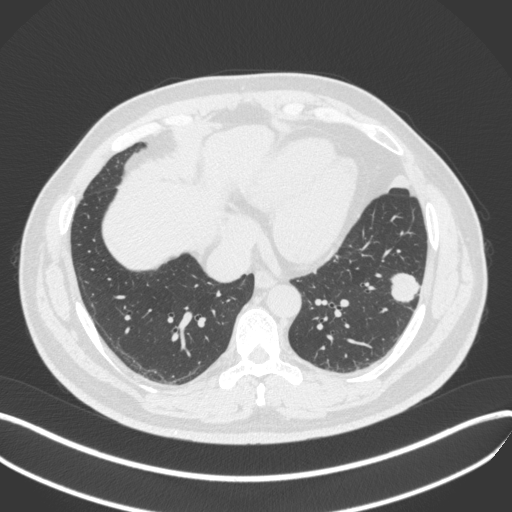
Chest CT, one axial slice; 120 kVp; lung window (W 1500 / L -600 HU); 1 mm slice thickness; 512 × 512 image matrix, field of view 400 × 400 mm. Male patient, age 39 years. Case-level facts recorded for this patient, not image findings: clinical TNM (as recorded): T2a N0 M0; histopathological grade: G2-3.
Outlined on this slice (bounding box drawn by a radiologist):
- lung tumour (recorded histology: adenocarcinoma): box from (x=387, y=271) to (x=424, y=308) px